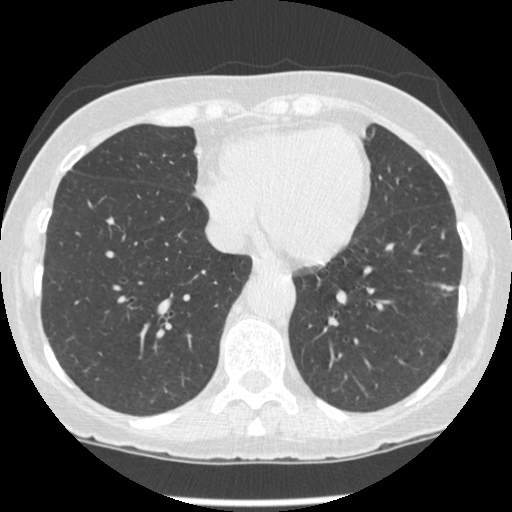
Low-dose screening chest CT, one axial slice. Position 81 of 247 along the scan axis. Reconstruction kernel STANDARD. Lung window (W 1500 / L -600 HU). 1.25 mm slice thickness. 512 × 512 image matrix, field of view 303 × 303 mm.
Structures marked on this image (expert manual segmentation):
- lesion 1 (tumor, lower lobe of left lung): bounding box <441,284,453,291> (left, top, right, bottom; pixels)